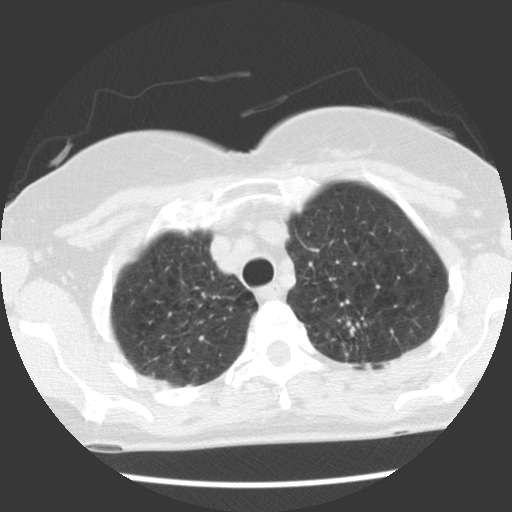
Low-dose screening chest CT, one axial slice. Position 95 of 120 along the scan axis. Reconstruction kernel STANDARD. 140 kVp. Lung window (W 1500 / L -600 HU). 512 × 512 image matrix, field of view 300 × 300 mm.
Outlined on this slice (manually delineated by an expert):
- lesion 1 (tumor, upper lobe of left lung): box from (x=350, y=328) to (x=355, y=335) px